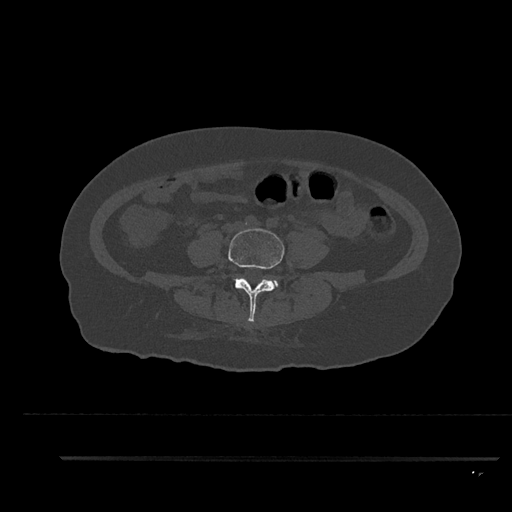
CT including the spine, one axial slice; slice 9 of 797 in the series (ordered by position); reconstruction kernel Br40s/3; 120 kVp; bone window (W 1800 / L 400 HU); 0.5 mm slice thickness; 512 × 512 image matrix, field of view 408 × 408 mm. Female patient, age 44 years. From the clinical record (not read from this slice): primary cancer: renal; vertebrae with lytic lesions (as recorded): L1.
Outlined on this slice (semi-automatically segmented with operator editing):
- L4 vertebra: bounding box <228,228,285,322> (left, top, right, bottom; pixels)